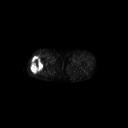
FDG PET of an extremity soft-tissue mass (from a PET/CT study), one axial slice; slice 245 of 267 in the series (ordered by position); 3.27 mm slice thickness; 128 × 128 image matrix, field of view 700 × 700 mm. Male patient, age 43 years. Case-level facts recorded for this patient, not image findings: histological type: poorly differentiated synovial sarcoma; grade: high; site of the primary tumour: right buttock.
Outlined on this slice (expert contour drawn on MRI and transferred to this co-registered scan by the dataset authors):
- gross tumour volume including surrounding oedema: bounding box [x1, y1, x2, y2] px = [30, 57, 43, 74]
- gross tumour volume (mass): [31, 57, 43, 74]